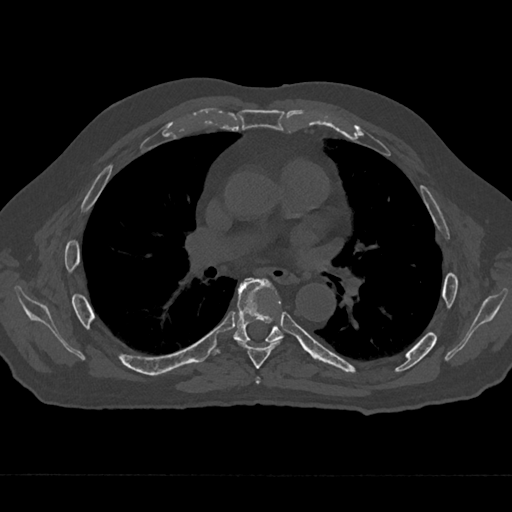
CT including the spine, one axial slice; position 398 of 797 along the scan axis; 120 kVp; bone window (W 1800 / L 400 HU); 0.5 mm slice thickness; 512 × 512 image matrix. Male patient, age 75 years. From the clinical record (not read from this slice): primary cancer: renal; vertebrae with lytic lesions (as recorded): T4.
Structures marked on this image (semi-automatically segmented with operator editing):
- T5 vertebra: bounding box <255,377,260,384> (left, top, right, bottom; pixels)
- T6 vertebra: <238,341,280,369>
- T7 vertebra: <211,278,284,355>